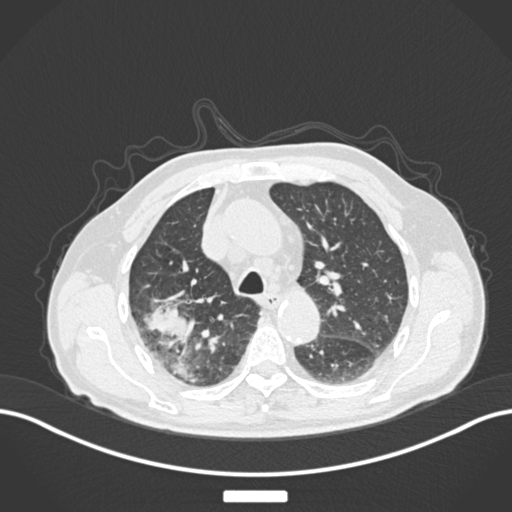
Chest CT, one axial slice; position 132 of 201 along the scan axis; reconstruction kernel B30f; 120 kVp; lung window (W 1500 / L -600 HU); 512 × 512 image matrix, field of view 400 × 400 mm. Patient: male, 72 years. Case-level facts recorded for this patient, not image findings: clinical TNM (as recorded): T3 N2 M0.
Annotated regions visible in this slice (rectangle marked by the reading radiologist):
- lung tumour (recorded histology: adenocarcinoma): bounding box <143,296,192,342> (left, top, right, bottom; pixels)